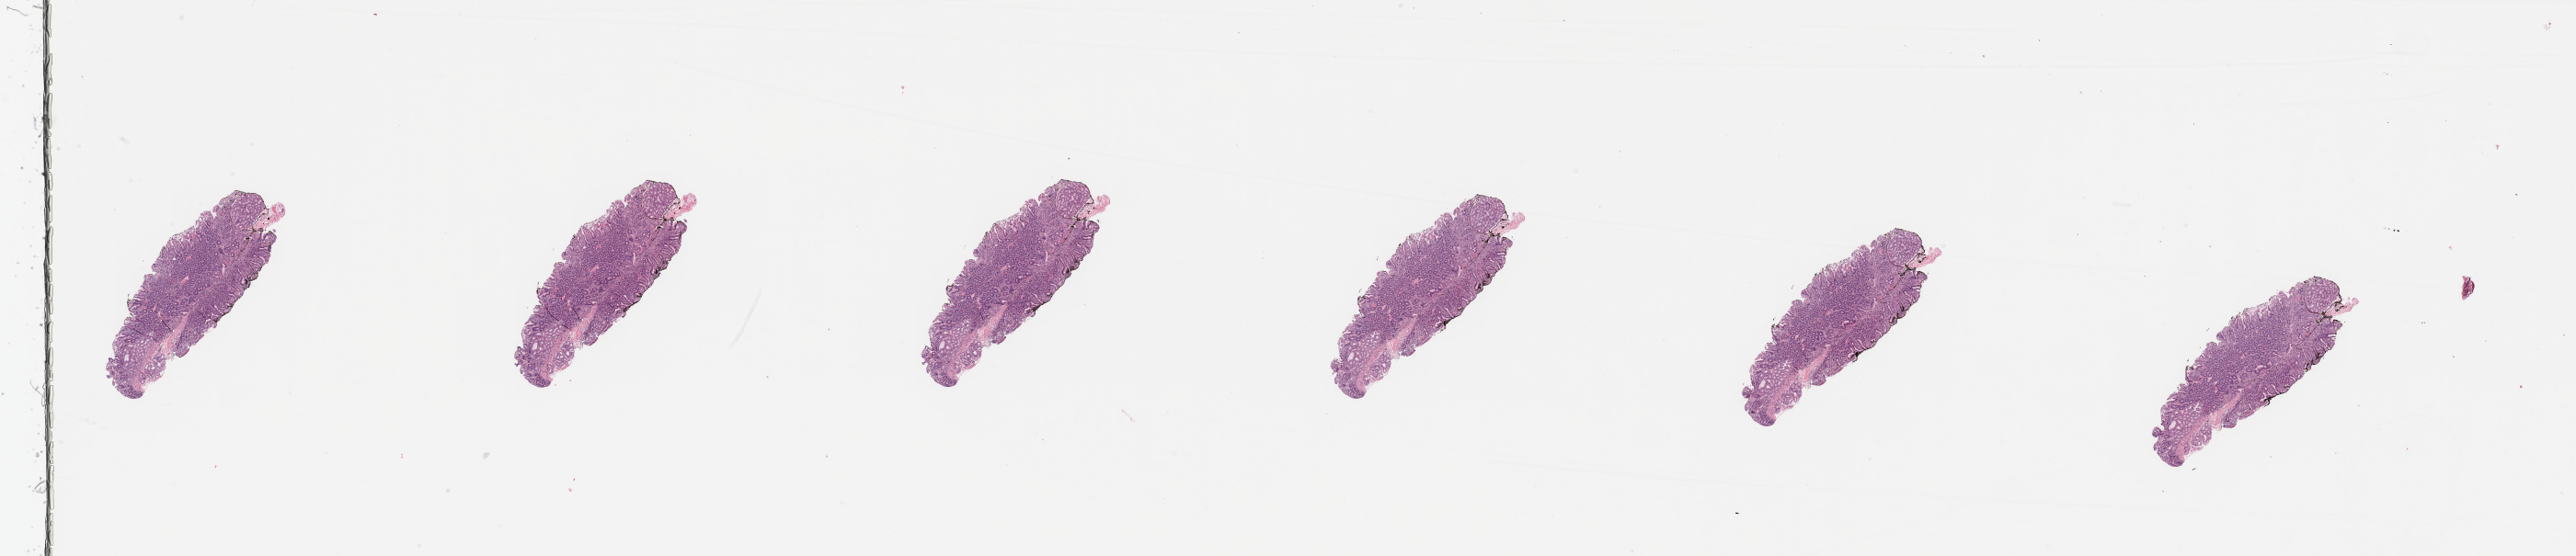
Whole-slide histology image, Hematoxylin and eosin (H&E) stained, whole scanned area (about 44.3 x 9.6 mm, from a 20x scan) shown as a low-resolution overview; pancreas, normal (non-tumour) tissue. 69-year-old female patient.
This section: normal (non-tumour) tissue from the same patient. Patient diagnosis: Infiltrating duct carcinoma, NOS.